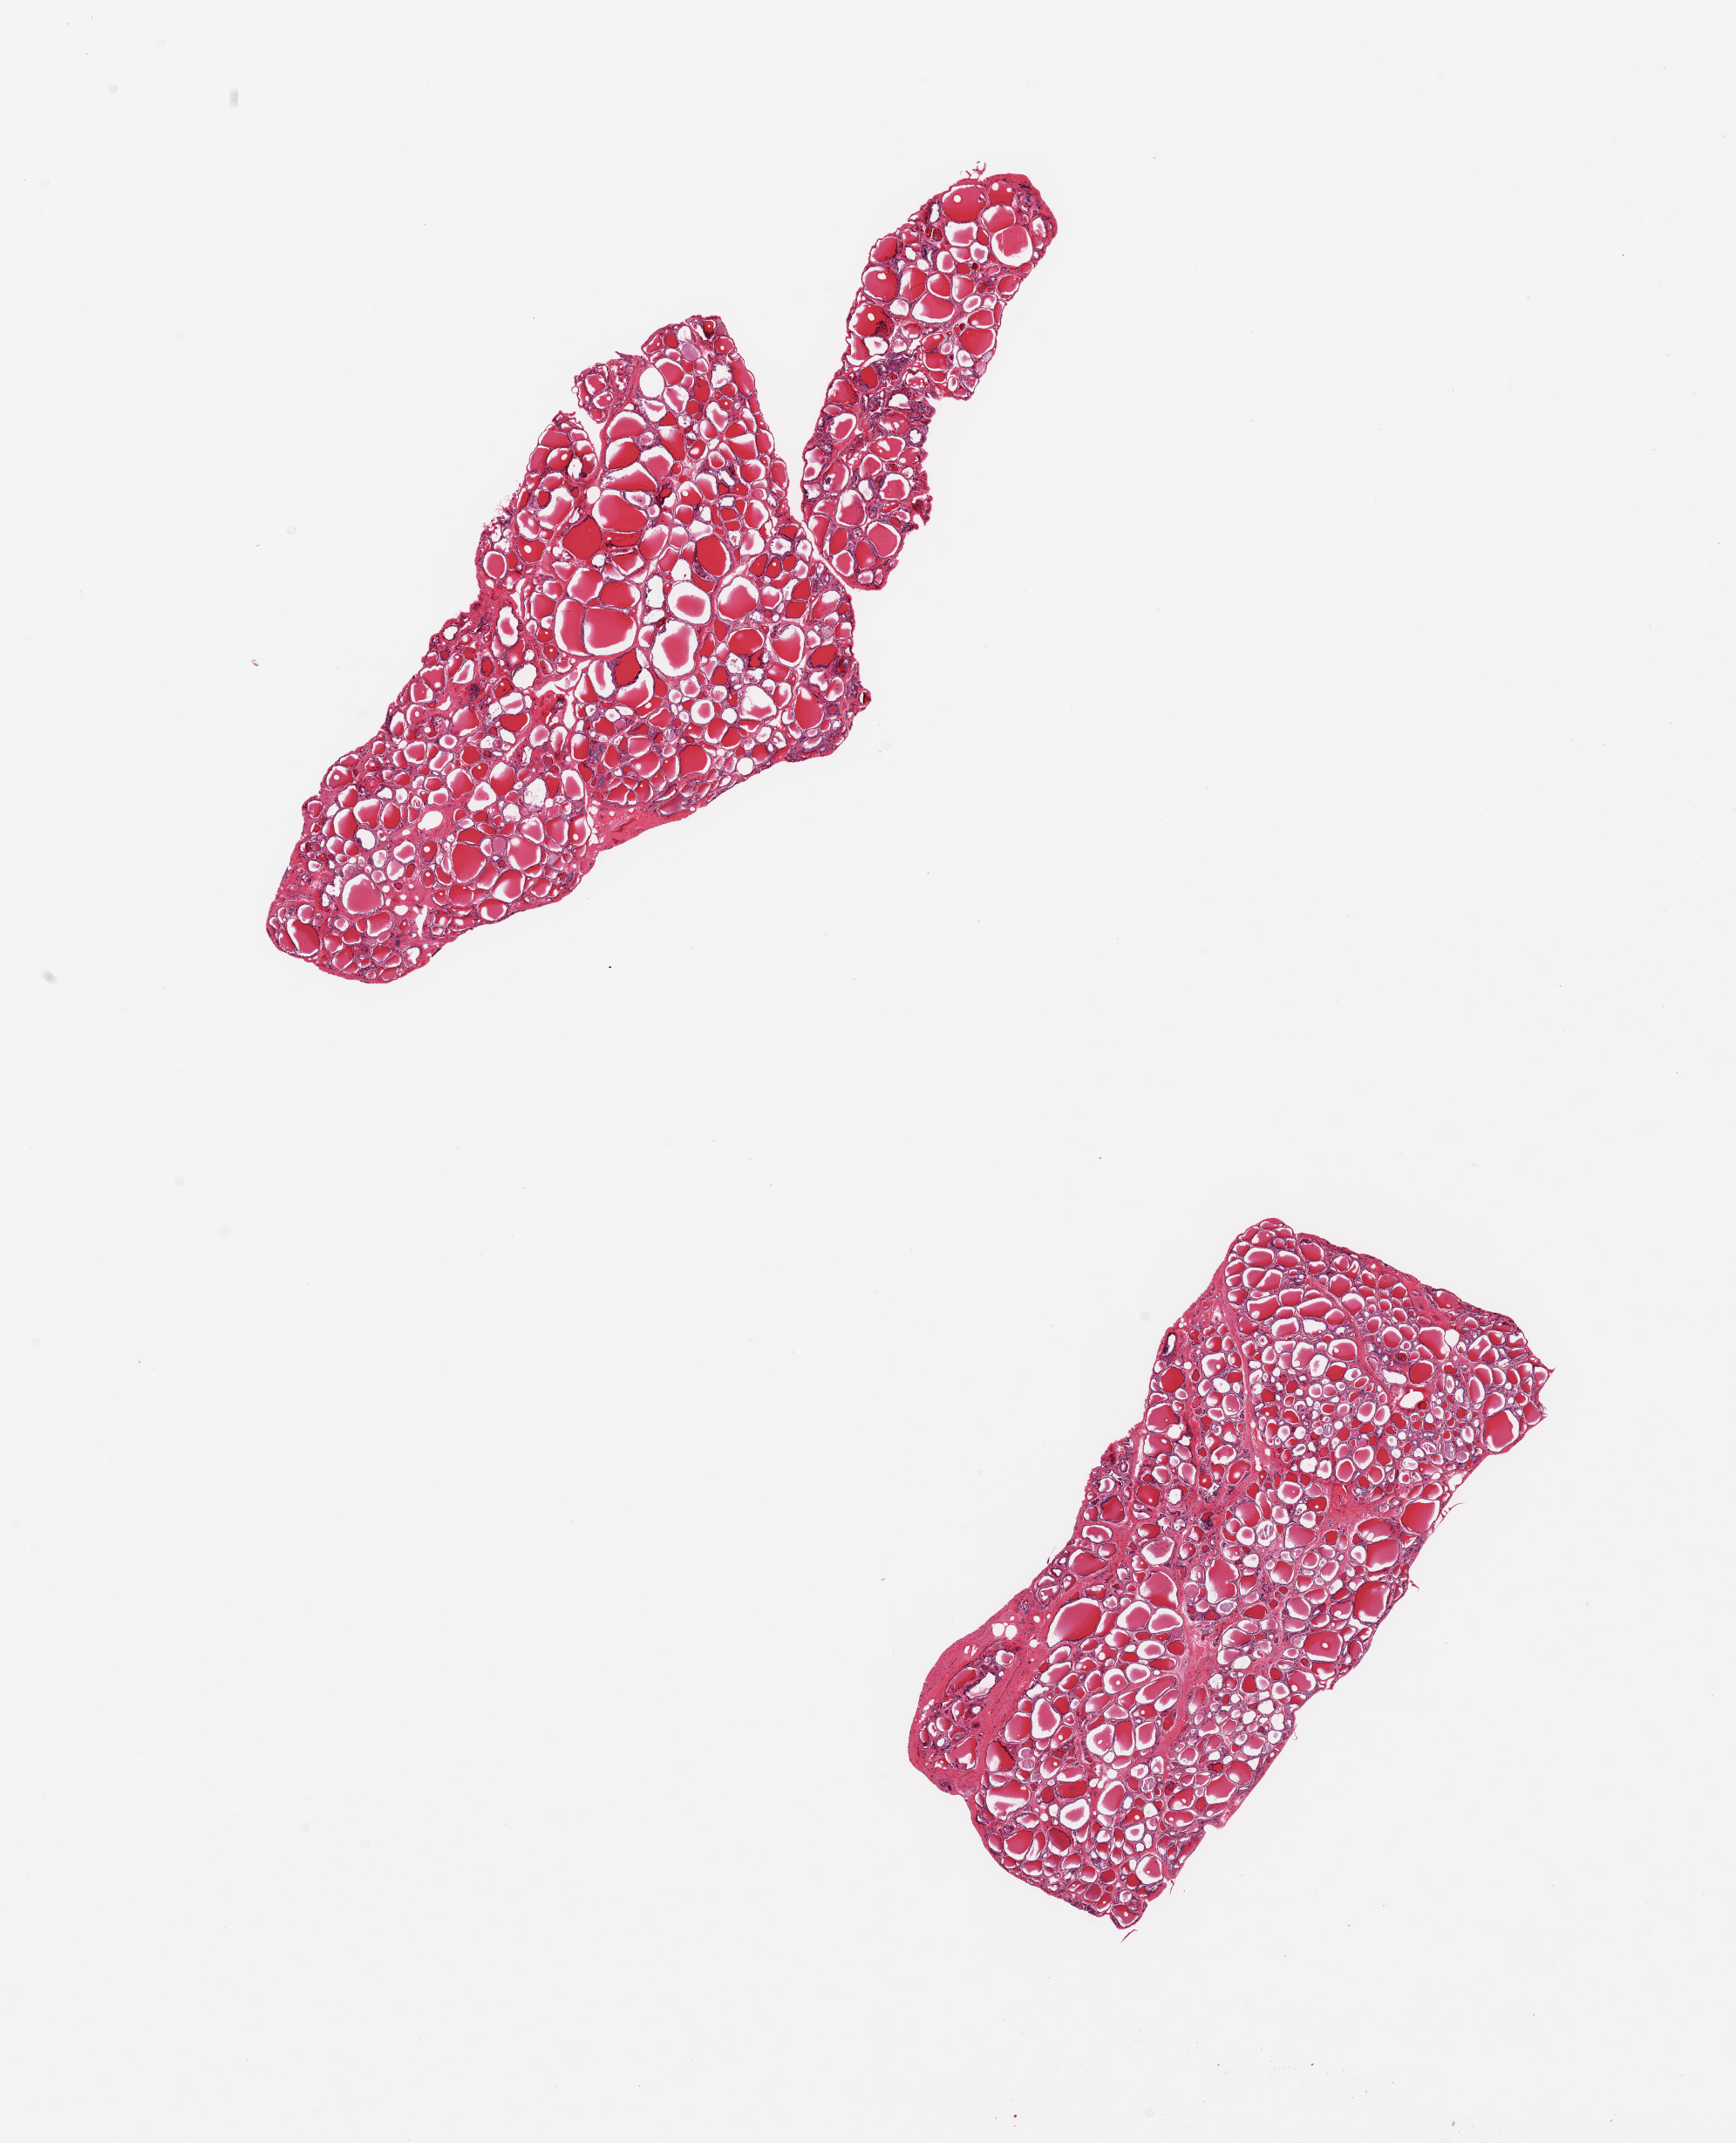
Whole-slide image, haematoxylin and eosin stain, brightfield, shown as a low-resolution overview of the whole scanned area (about 15.8 x 19.4 mm), PAXgene-fixed paraffin-embedded (PFPE) section, section of thyroid (target tissue), donor tissue sample. Donor: male.
* review note (as recorded): 2 pieces; 5% stromal content